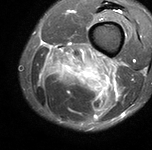
MRI of an extremity soft-tissue mass, one axial slice; position 24 of 90 along the scan axis; STIR; MR volume resampled by the dataset authors to the PET/CT grid (not the native acquisition matrix); 3.27 mm slice thickness; 152 × 150 image matrix, field of view 148 × 146 mm. Male patient. Case-level facts recorded for this patient, not image findings: histological type: undifferentiated pleomorphic liposarcoma; grade: high; site of the primary tumour: left thigh.
Outlined on this slice (expert contour drawn on MRI and transferred to this co-registered scan by the dataset authors):
- gross tumour volume including surrounding oedema: bounding box (x1, y1, x2, y2) in pixels: (39, 43, 124, 111)